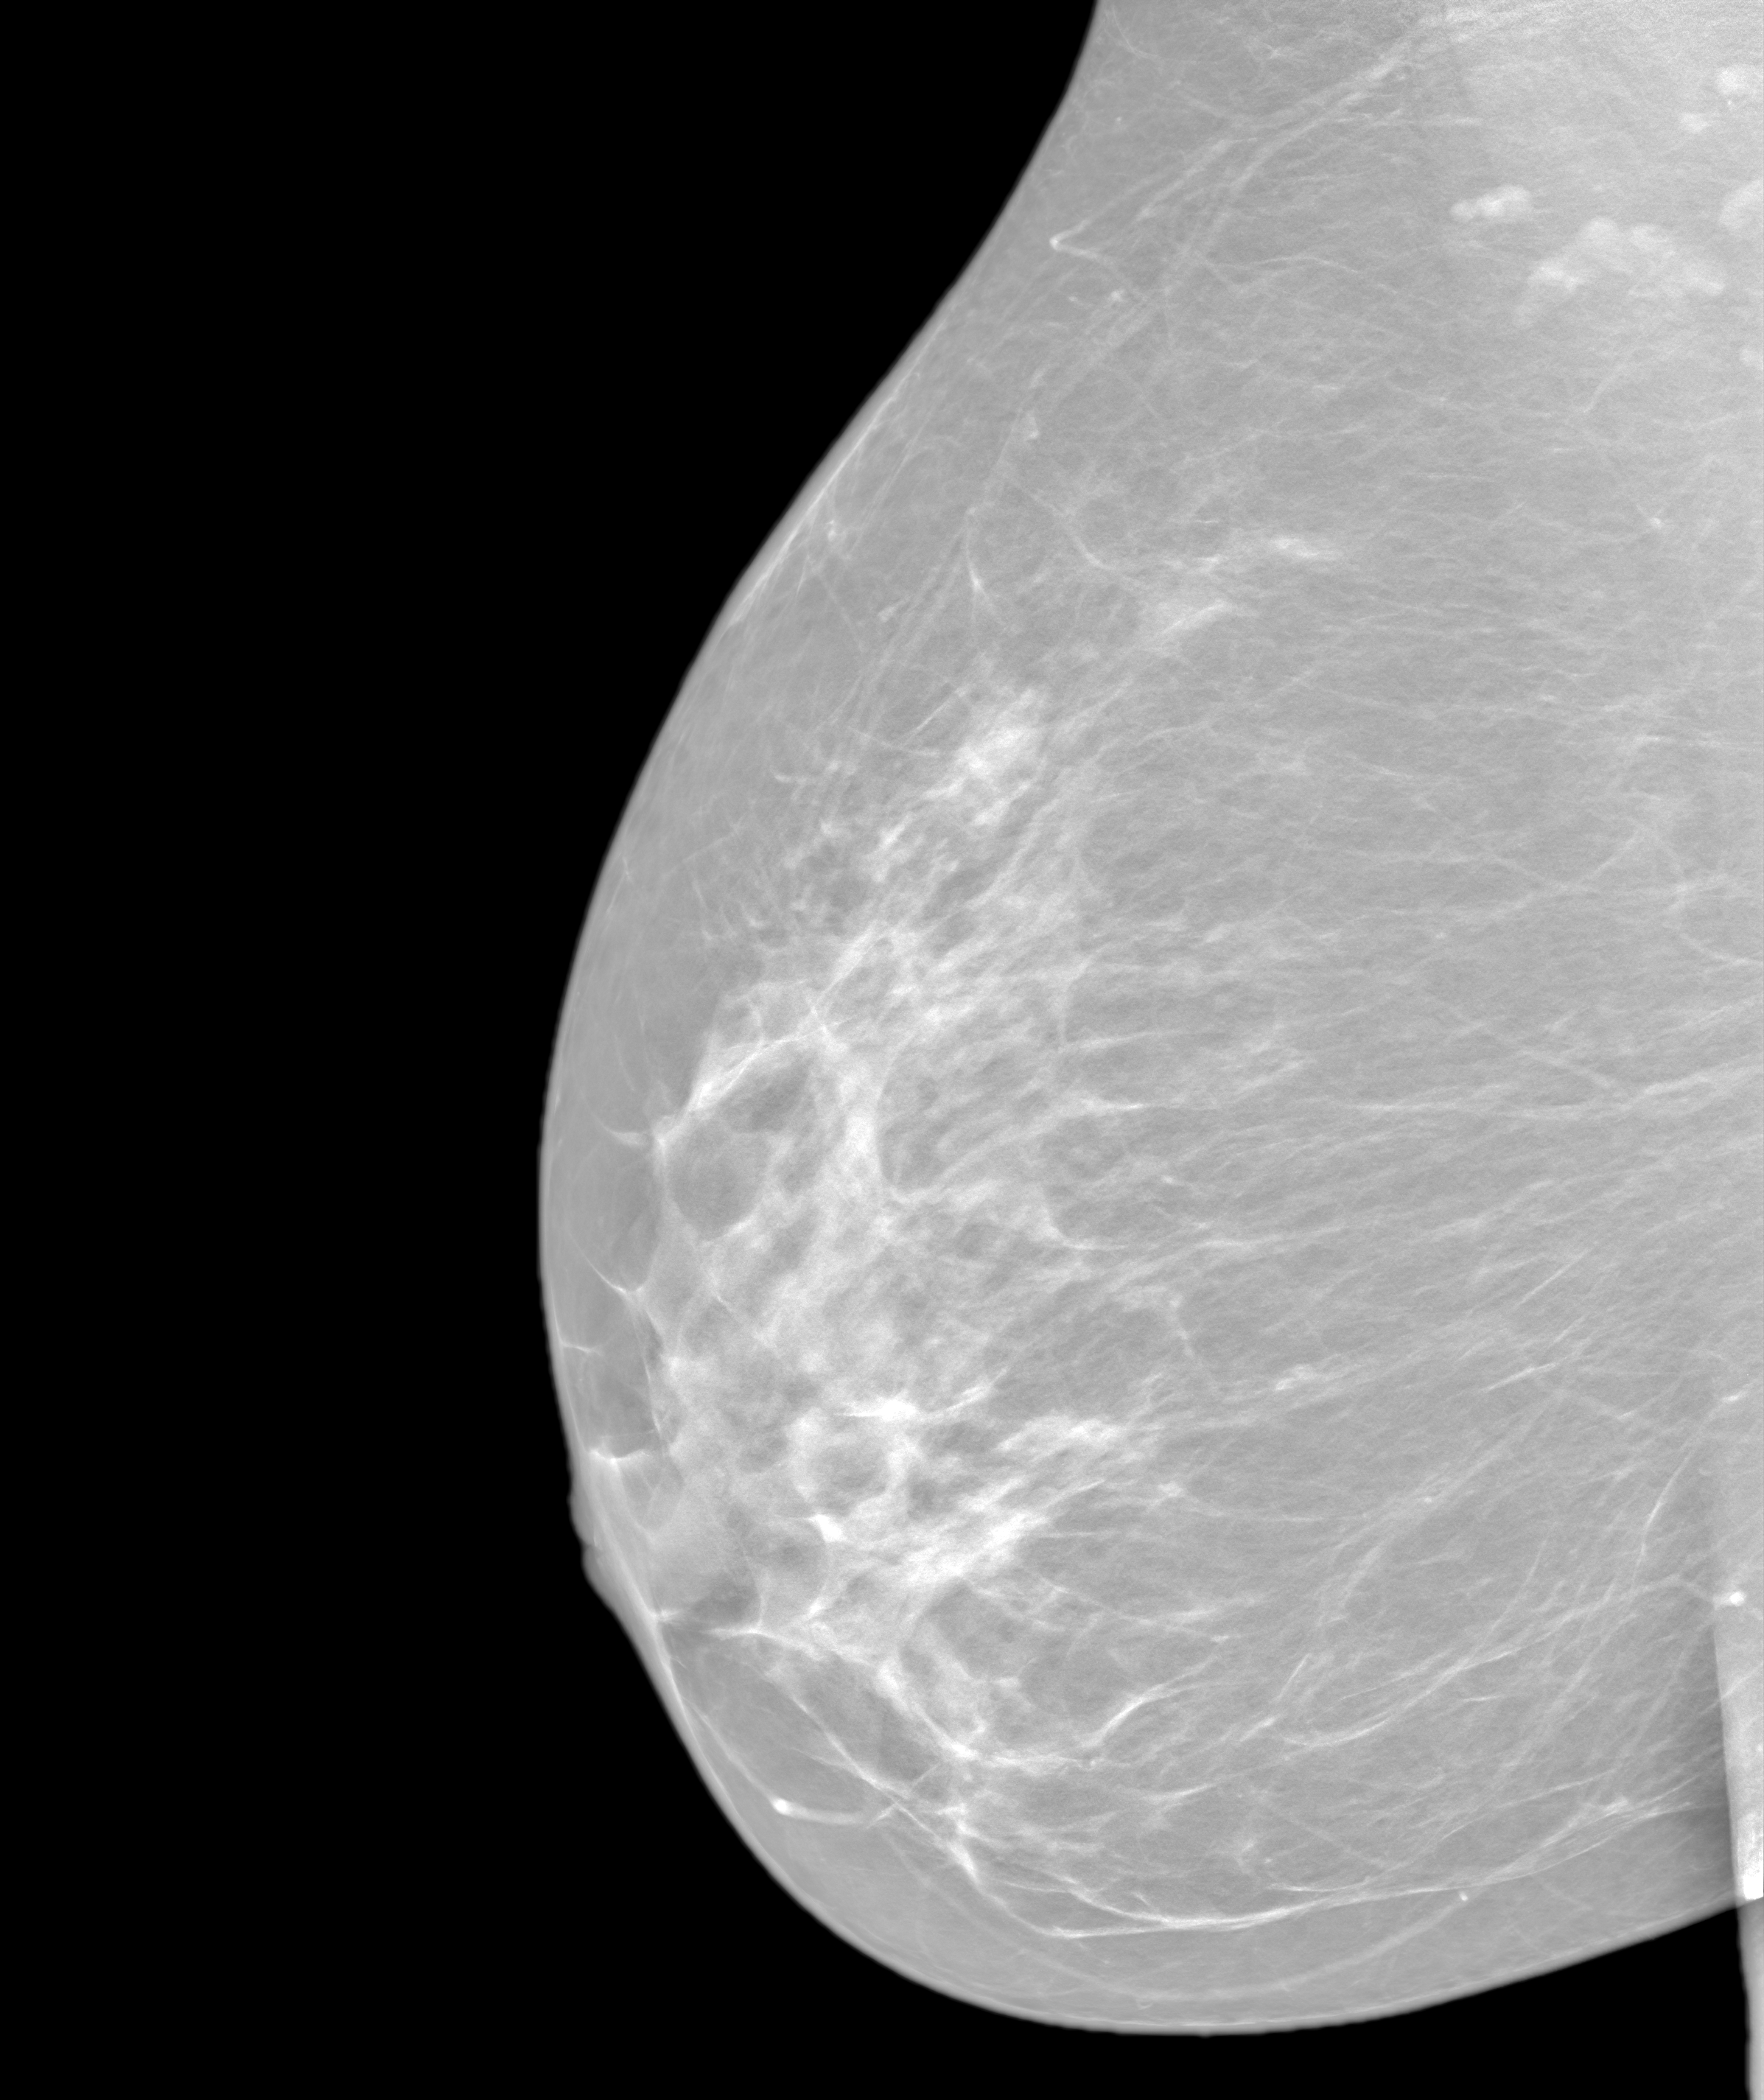
Screening examination, system: SenoIris_1SP2(440). Female patient, age 57 years.
Image type: synthesized 2-D view from tomosynthesis. Breast: right. Projection: MLO view.